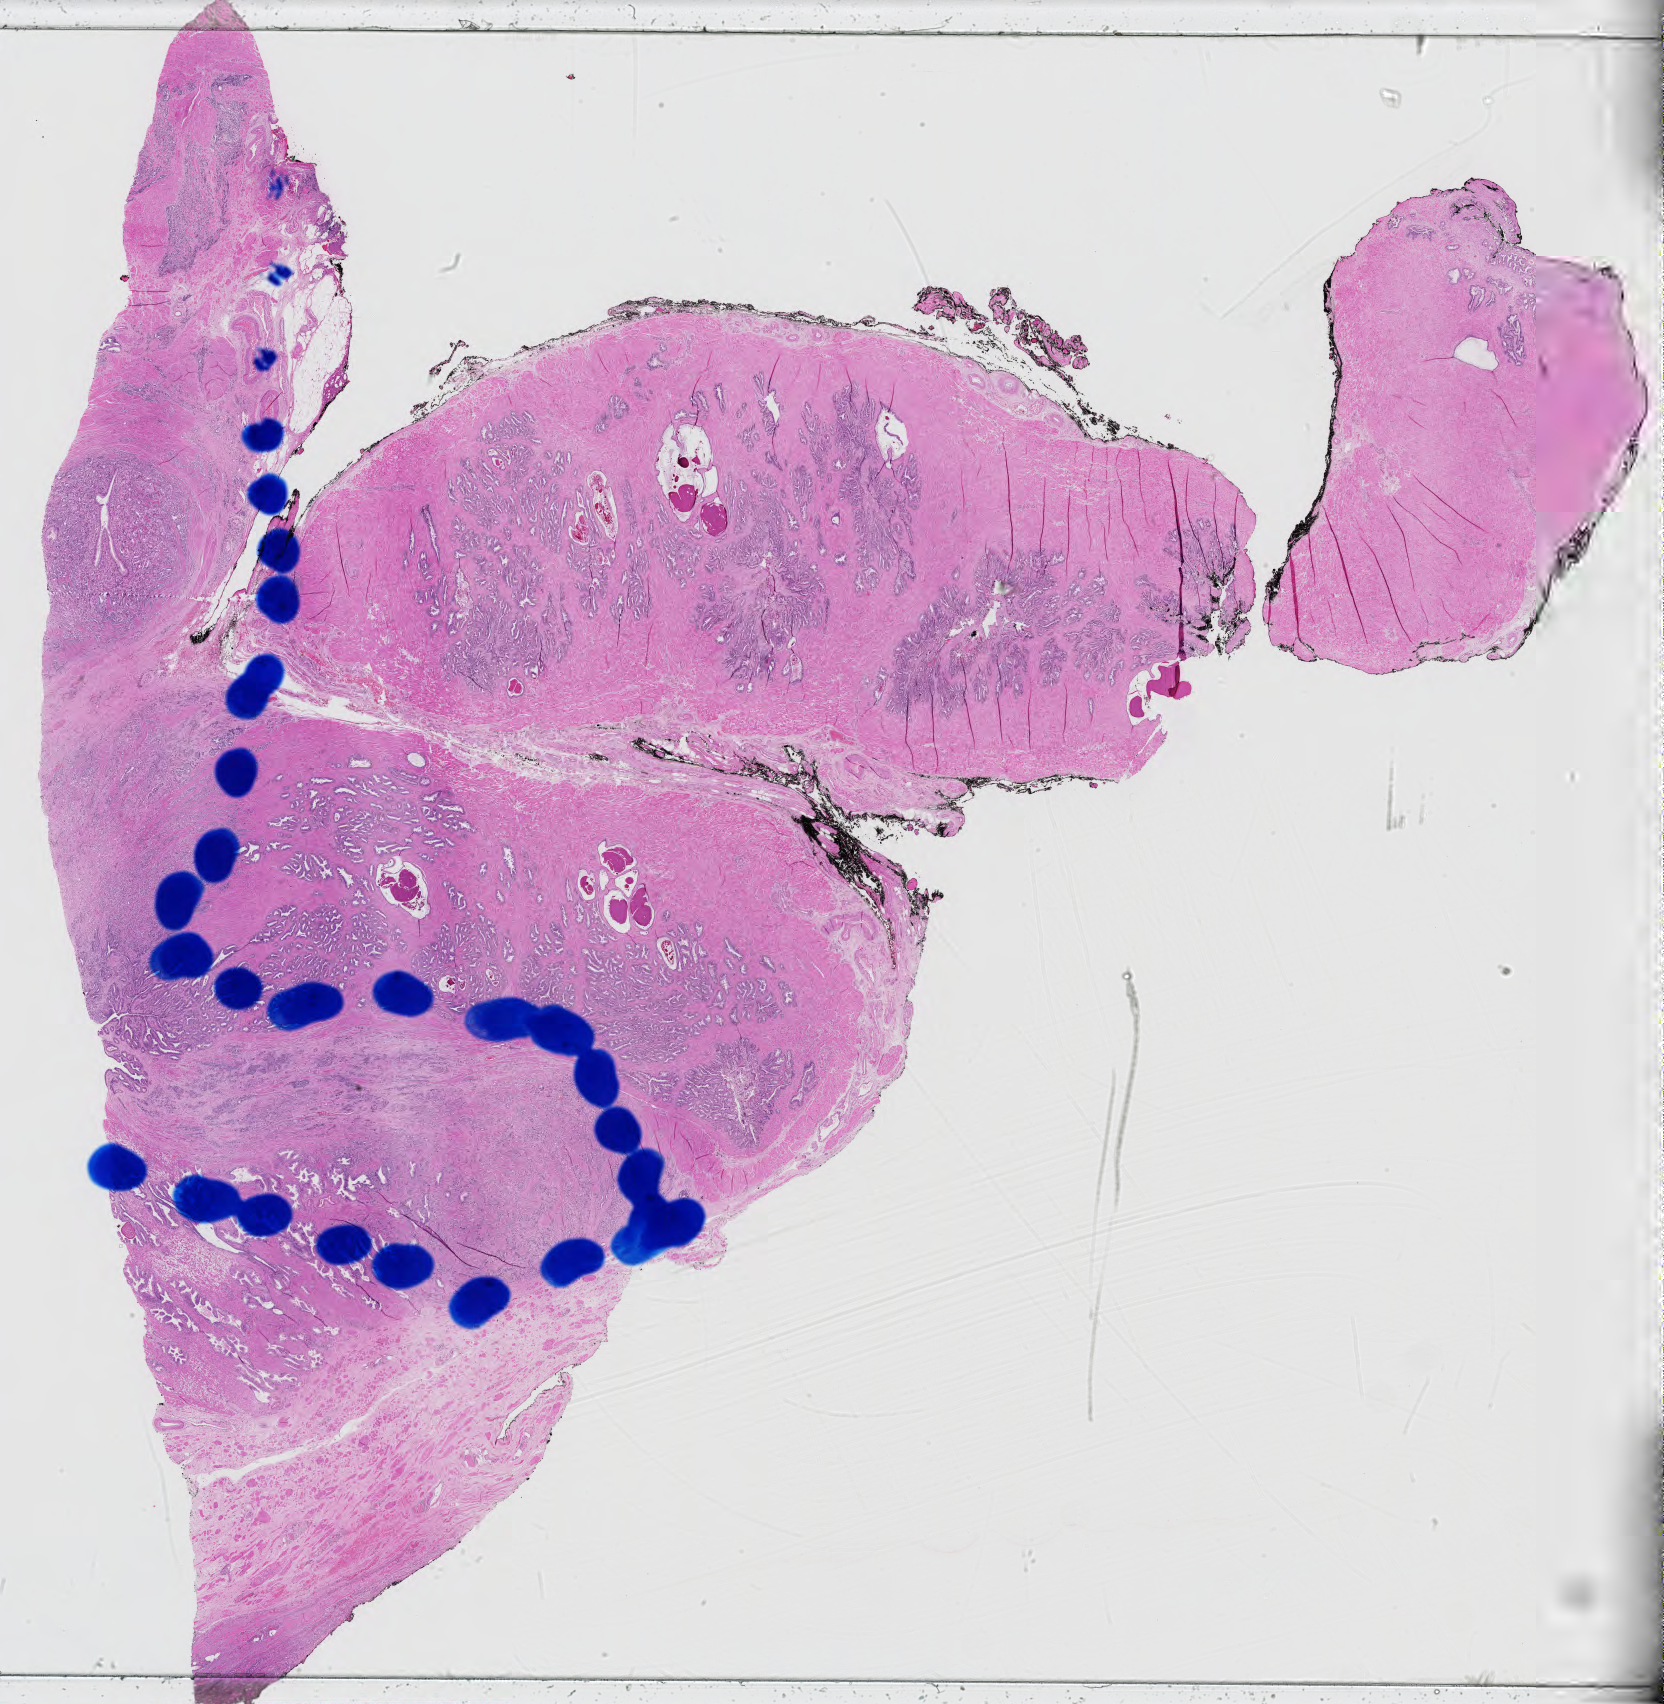
Digitized Hematoxylin and eosin (H&E) stained tissue section (whole slide), a low-resolution overview of the entire scanned area, about 24.1 x 24.7 mm, formalin-fixed paraffin-embedded (FFPE) diagnostic section, primary tumour sample from the prostate. Male, age 60 years at initial diagnosis. Gleason score: 9 (4+5).
- pathologic diagnosis: Adenocarcinoma, NOS (prostate gland)
- lymph nodes positive (case pathology): 0 of 29 examined